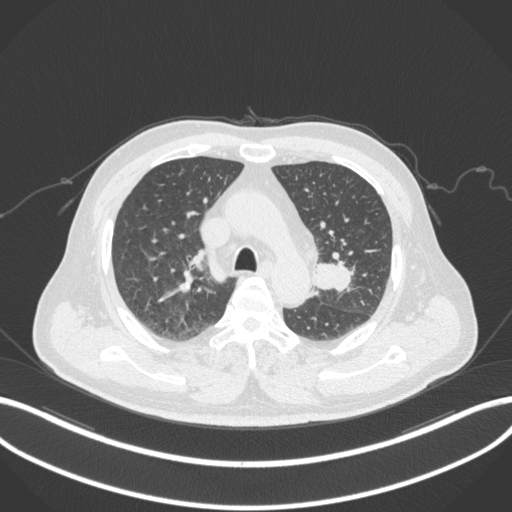
Chest CT, one axial slice. Position 208 of 286 along the scan axis. 120 kVp. Lung window (W 1500 / L -600 HU). 1 mm slice thickness. 512 × 512 image matrix, field of view 400 × 400 mm. Patient: male, 67 years. From the clinical record (not read from this slice): clinical TNM (as recorded): T2a N1 M0; histopathological grade: G3.
Outlined on this slice (rectangle marked by the reading radiologist):
- lung tumour (recorded histology: adenocarcinoma): bounding box <308,257,354,294> (left, top, right, bottom; pixels)